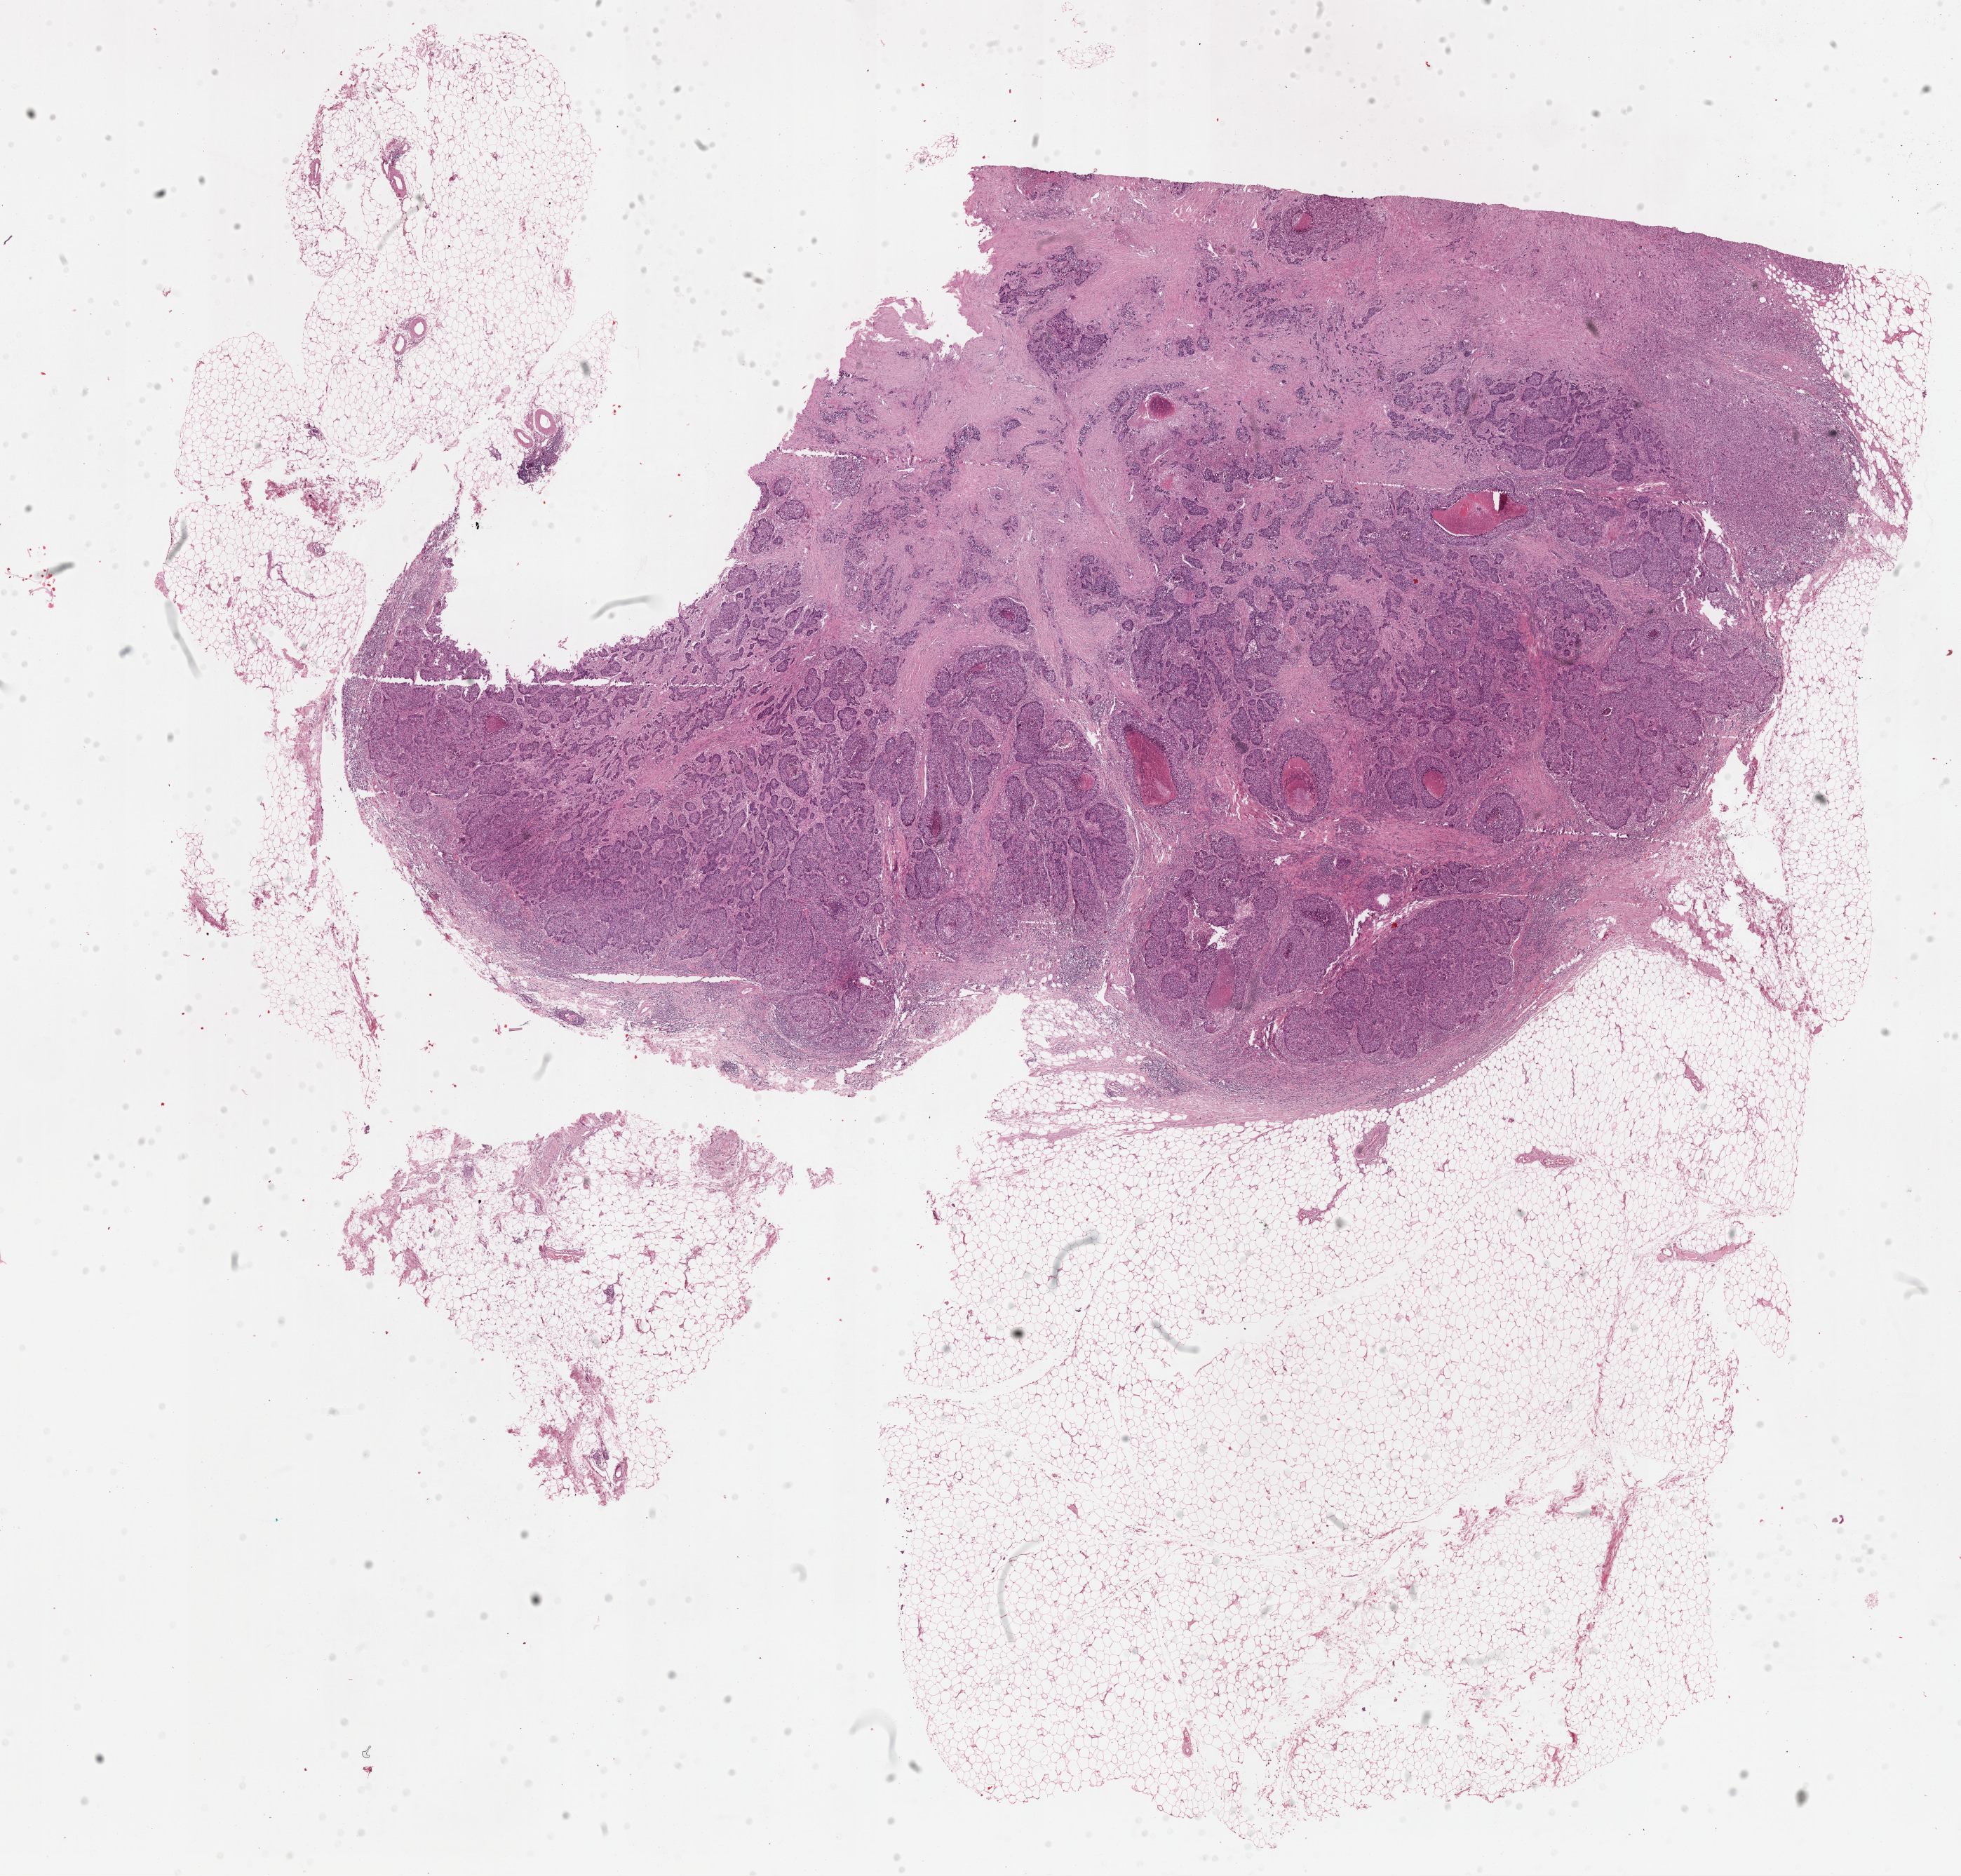
Whole-slide histology image, H&E-stained, low-resolution overview of the scanned area, about 22.1 x 21.1 mm. Formalin-fixed paraffin-embedded (FFPE) diagnostic section. Sample: primary tumour, breast. Female patient; age at initial diagnosis 69 years.
- AJCC pathologic stage: IIA
- pathologic diagnosis: Infiltrating duct carcinoma, NOS